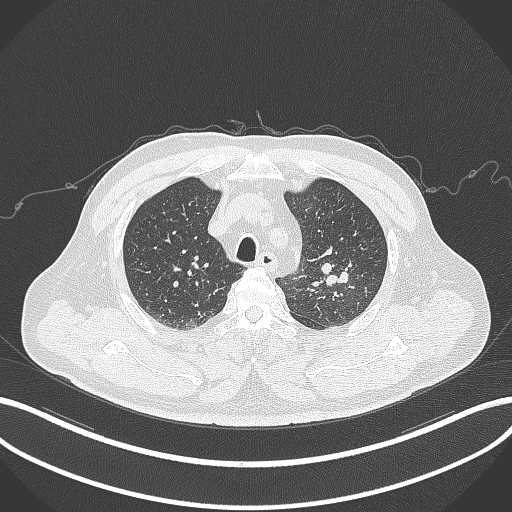
Chest CT, one axial slice; position 241 of 286 along the scan axis; reconstruction kernel B70f; 120 kVp; lung window (W 1500 / L -600 HU); 1 mm slice thickness; 512 × 512 image matrix, field of view 400 × 400 mm. Patient: male, 67 years. From the clinical record (not read from this slice): clinical TNM (as recorded): T2a N1 M0; histopathological grade: G3.
Outlined on this slice (bounding box drawn by a radiologist):
- lung tumour (recorded histology: adenocarcinoma): bounding box [x1, y1, x2, y2] px = [318, 256, 350, 289]